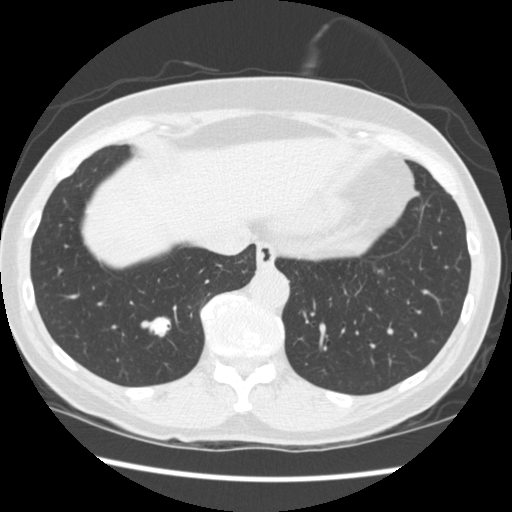
Low-dose screening chest CT, one axial slice. Position 66 of 262 along the scan axis. Reconstruction kernel STANDARD. 120 kVp. Lung window (W 1500 / L -600 HU). 512 × 512 image matrix, field of view 340 × 340 mm.
Structures marked on this image (outlined manually by an expert reader):
- lesion 1 (tumor, lower lobe of right lung): bounding box (x1, y1, x2, y2) in pixels: (150, 317, 170, 337)